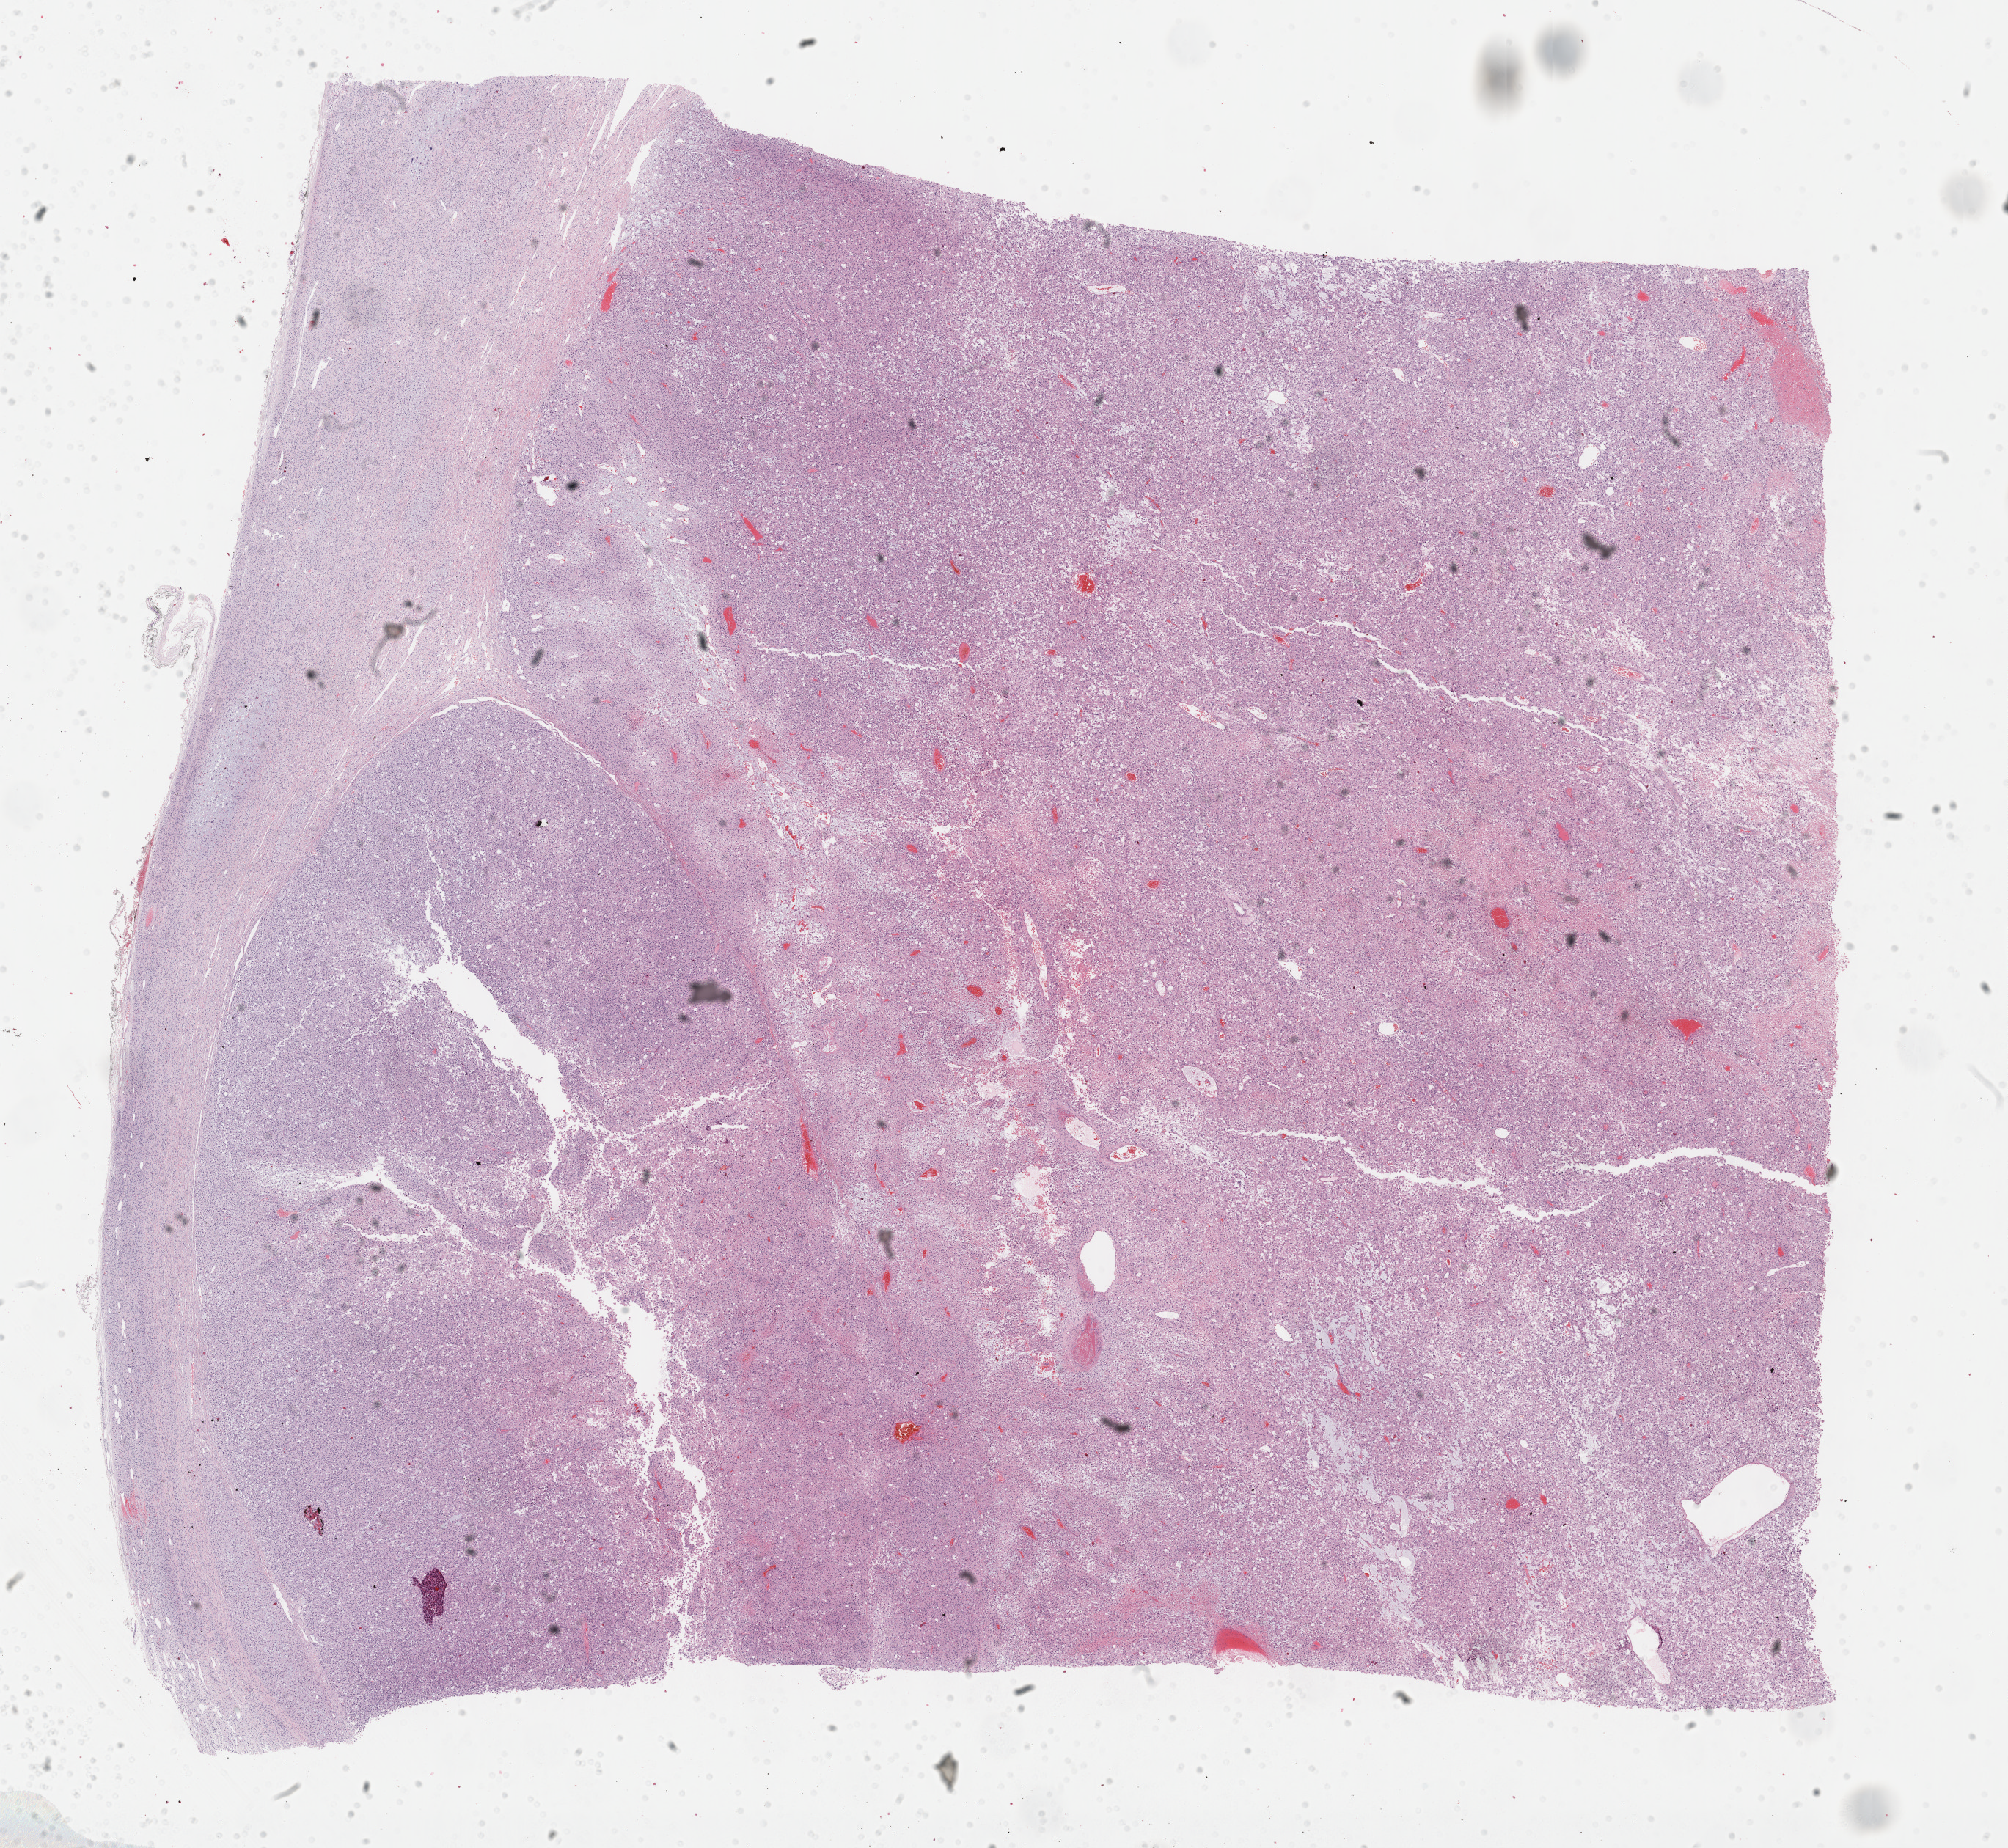
Whole-slide histology image, Hematoxylin and eosin (H&E) stained — a low-resolution overview of the entire scanned area, about 22.1 x 20.4 mm. Formalin-fixed paraffin-embedded (FFPE) diagnostic section. Adrenal cortex, primary tumour sample. Male patient; age at initial diagnosis 40 years.
* diagnosis: Adrenal cortical carcinoma (cortex of adrenal gland)